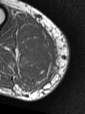
MRI of an extremity soft-tissue mass, one axial slice; slice 33 of 47 in the series (ordered by position); MR volume resampled by the dataset authors to the PET/CT grid (not the native acquisition matrix); 3.27 mm slice thickness; 85 × 114 image matrix. Male patient. Case-level facts recorded for this patient, not image findings: histological type: pleiomorphic liposarcoma; grade: high; site of the primary tumour: right calf.
Structures marked on this image (expert contour drawn on MRI and transferred to this co-registered scan by the dataset authors):
- gross tumour volume including surrounding oedema: bounding box [x1, y1, x2, y2] px = [22, 28, 57, 72]
- gross tumour volume (mass): [33, 41, 50, 56]